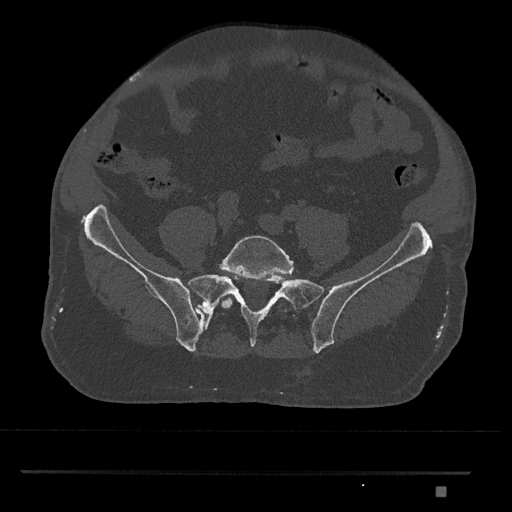
CT including the spine, one axial slice. Position 525 of 1134 along the scan axis. Reconstruction kernel Br40s/3. Bone window (W 1800 / L 400 HU). 512 × 512 image matrix. Male patient, age 65 years. Case-level facts recorded for this patient, not image findings: primary cancer: prostate.
Annotated regions visible in this slice (semi-automatically segmented with operator editing):
- L5 vertebra: bounding box [x1, y1, x2, y2] px = [220, 235, 294, 310]